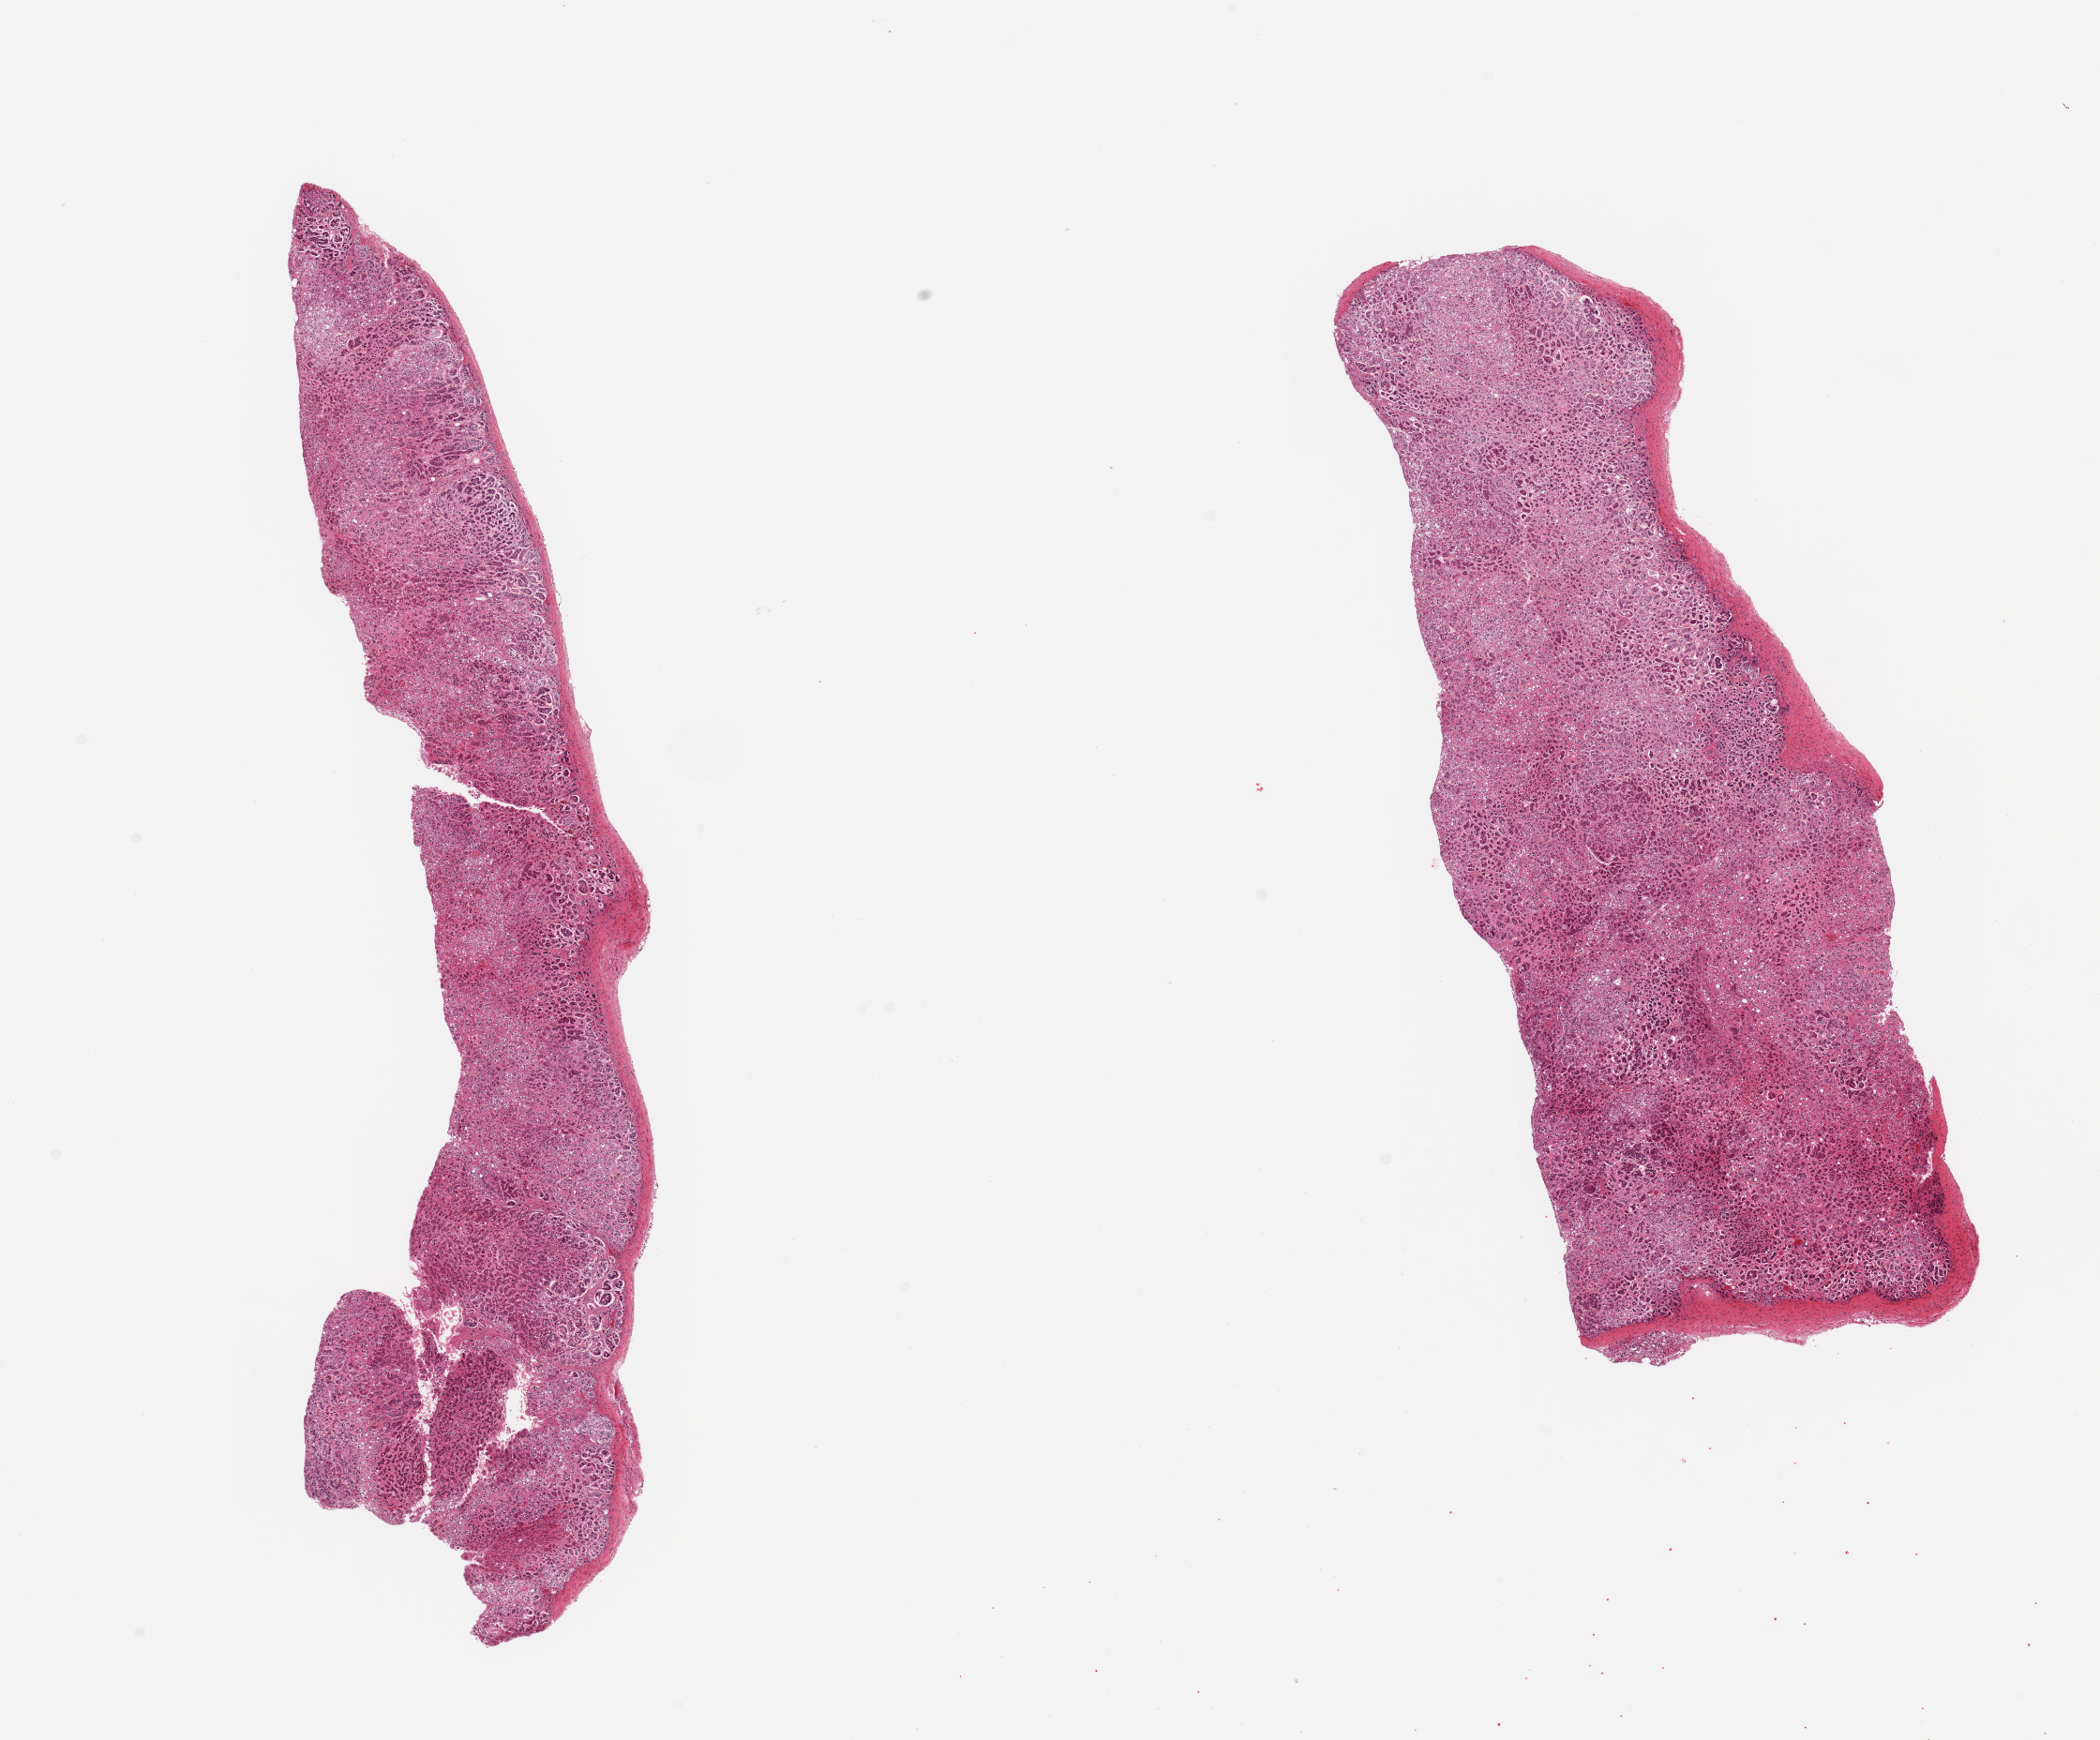
Hematoxylin and eosin (H&E) whole-slide image — shown as a low-resolution overview of the whole scanned area (about 17.7 x 14.7 mm). PAXgene-fixed, paraffin-embedded tissue. Sampled site (target tissue): adrenal gland. Tissue donor sample. Donor sex: male.
* review note (as recorded): 2 pieces, cortex, moderate-advanced autolysis